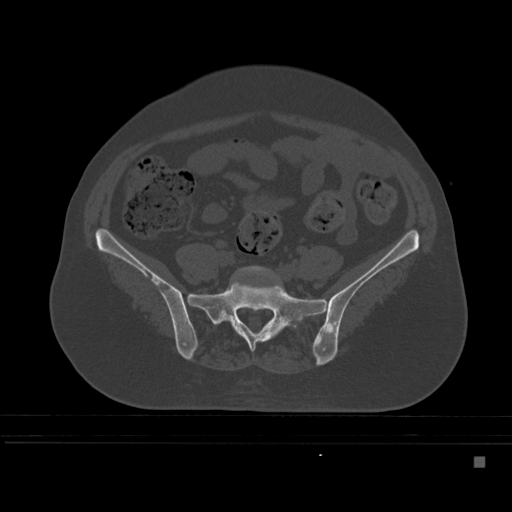
CT including the spine, one axial slice; position 96 of 495 along the scan axis; bone window (W 1800 / L 400 HU); 1.5 mm slice thickness; 512 × 512 image matrix, field of view 404 × 404 mm. Female patient, age 33 years. Case-level facts recorded for this patient, not image findings: primary cancer: breast.
Outlined on this slice (semi-automatically segmented with operator editing):
- L5 vertebra: bounding box <234,265,291,297> (left, top, right, bottom; pixels)